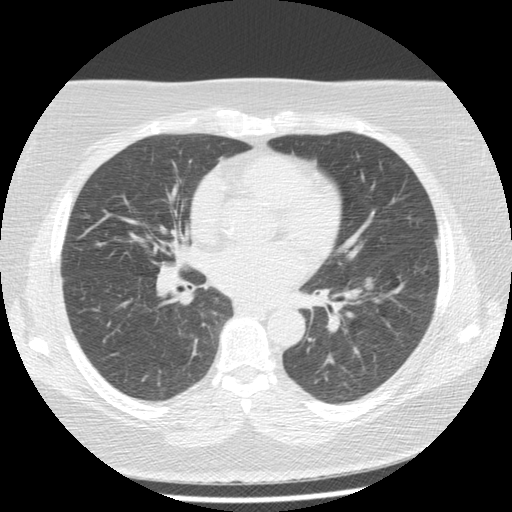
Axial slice from a low-dose chest CT screening exam; second screening round (one year after baseline); lung window (W 1500 / L -600 HU); 2.5 mm slice thickness; standard (soft-tissue) reconstruction kernel (STANDARD); 120 kVp; slice 76 of 157 in the series; 512 × 512 image matrix. Female participant, aged 65 years at enrolment.
Lesion marked by an expert reader, bounding box (x1, y1, x2, y2) in pixels: (350, 270, 382, 300). The exam's reader record, not a measurement of the box and not confirmed to be the same lesion: non-calcified nodule or mass ≥4 mm, left lower lobe, 9 × 7 mm, poorly defined margins, soft tissue attenuation, pre-existing on the prior screen: yes; interval growth: yes. Official screen result: positive, other. Lung cancer was diagnosed 651 days after this screen (after the third annual screen): adenocarcinoma, NOS, left lower lobe, moderately differentiated (G2), stage IA (AJCC 6th edition), 12 mm at pathology.